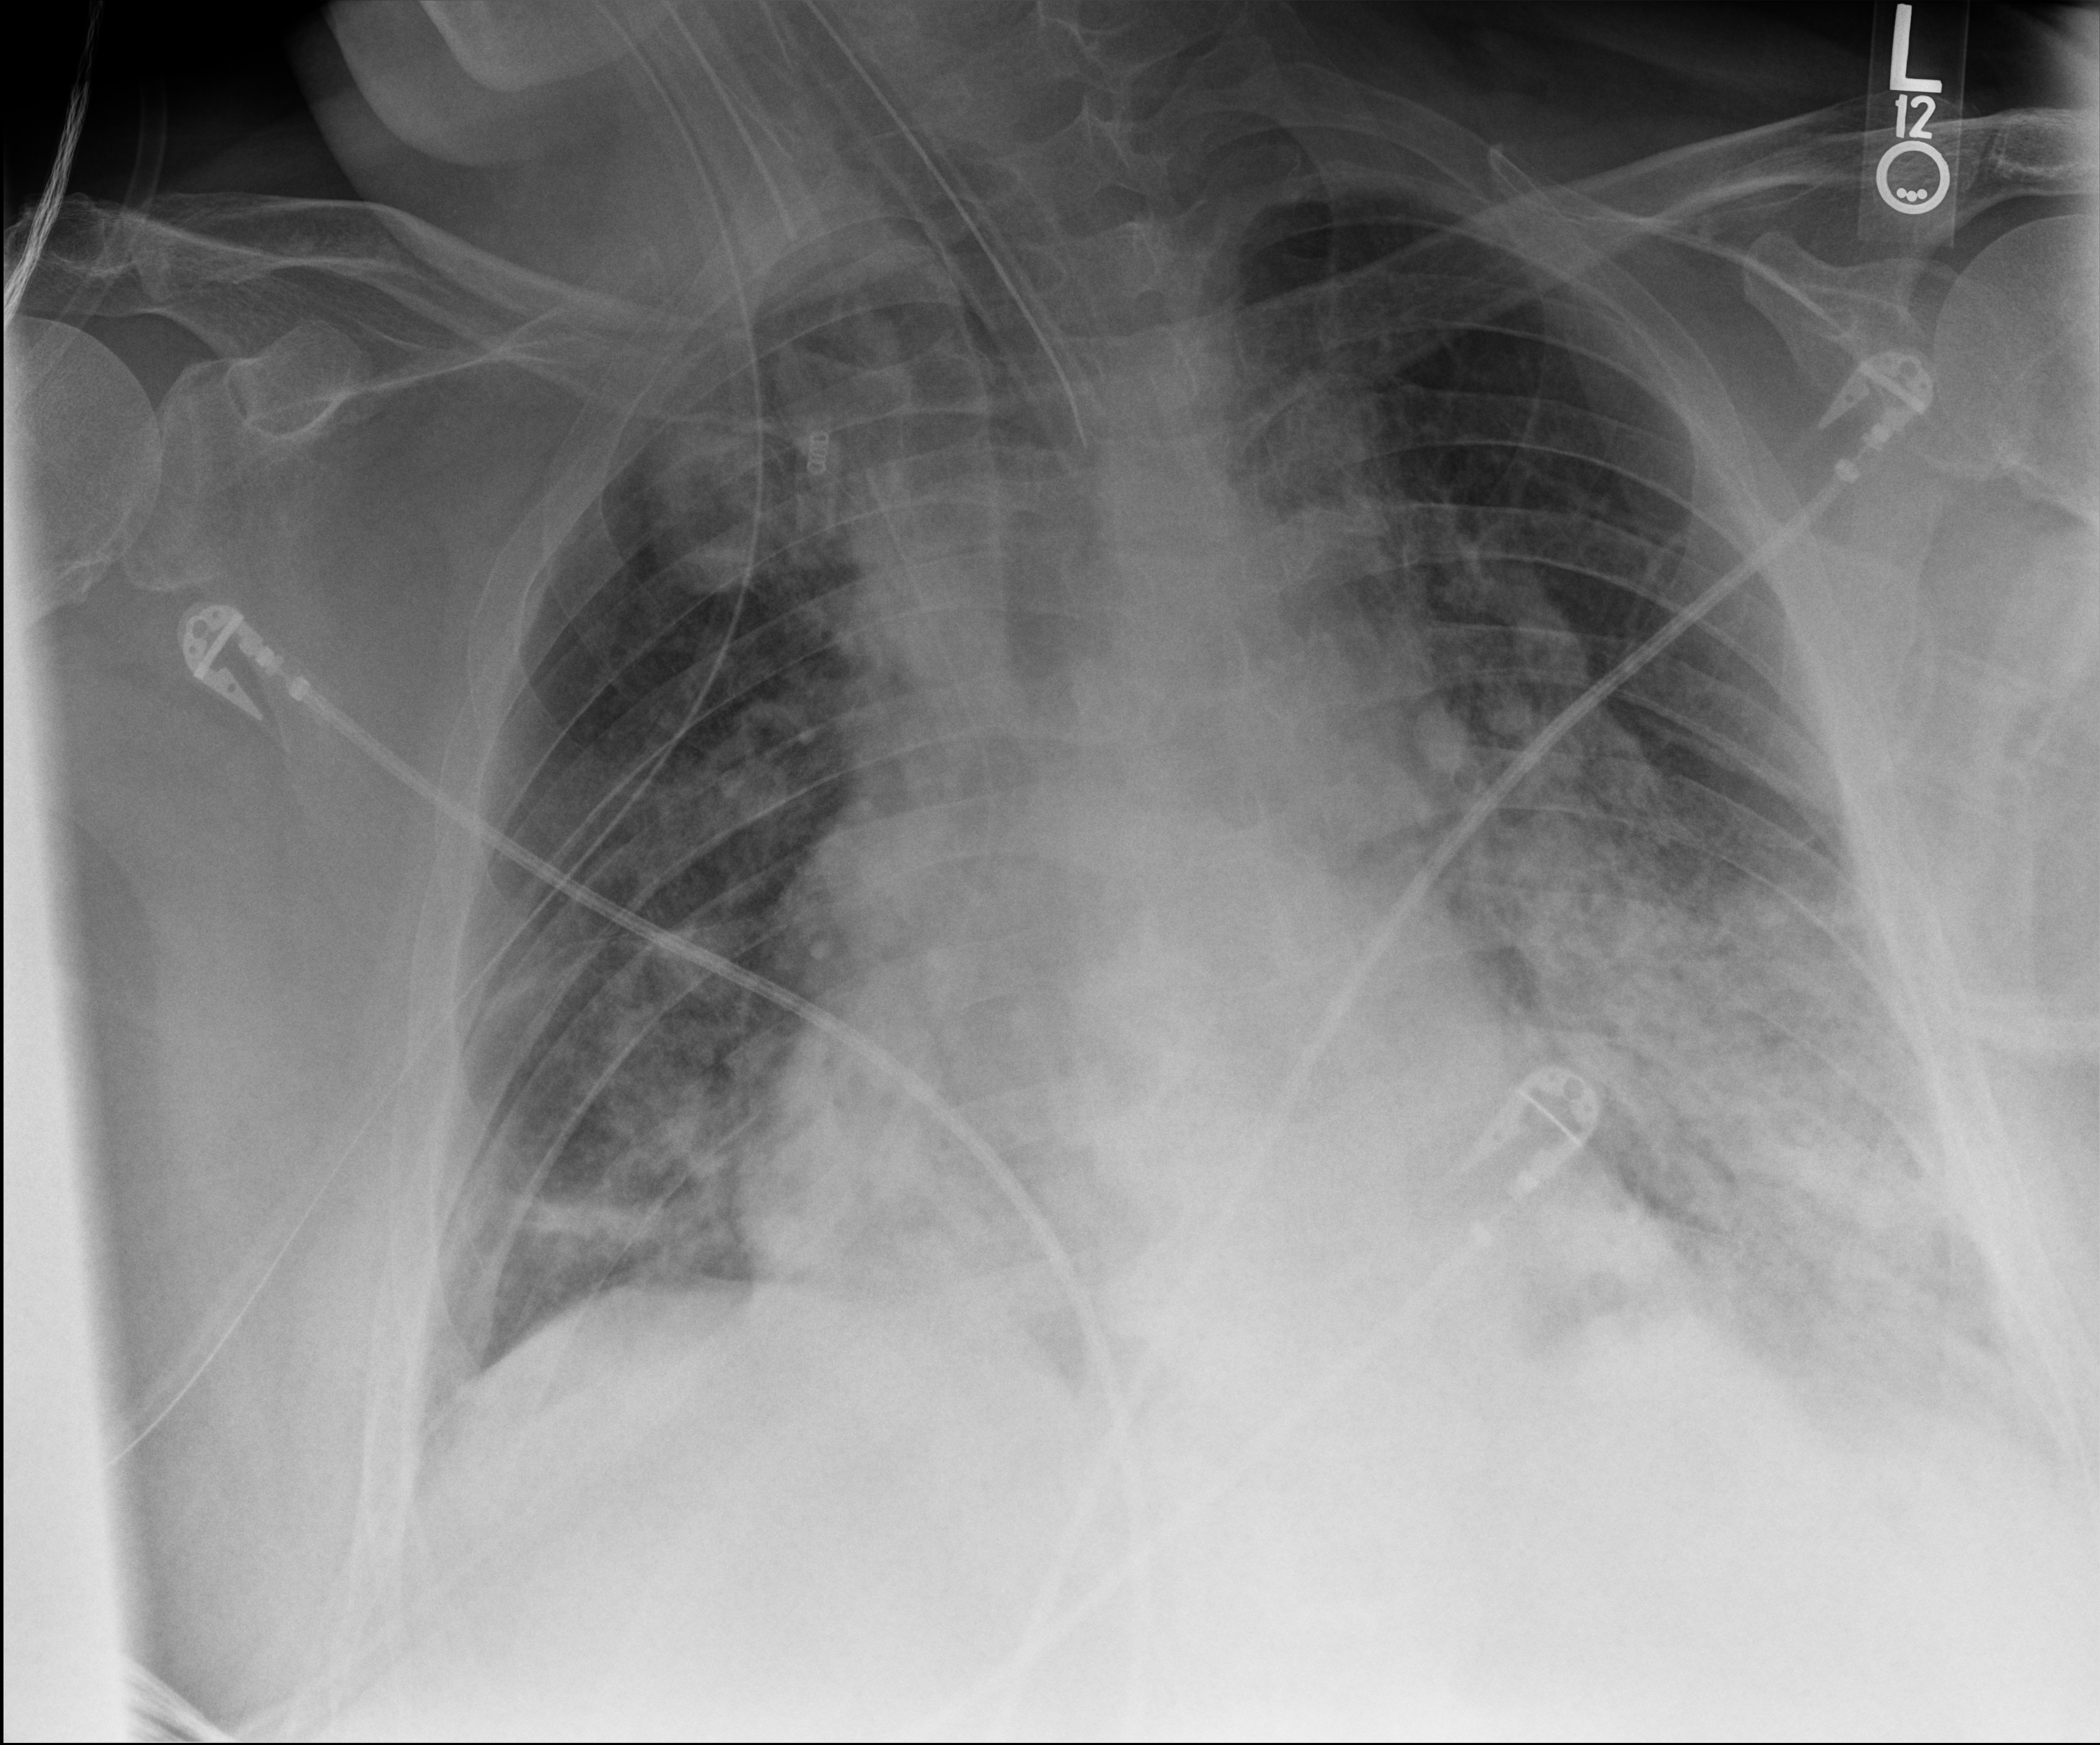
Chest radiograph, anteroposterior (AP) projection. Patient hospitalised with COVID-19; male, aged 60–74 years.
From the hospital-stay record, not from the radiograph (when in the stay this image was taken is not recorded):
- other chronic lung disease (admission record): yes